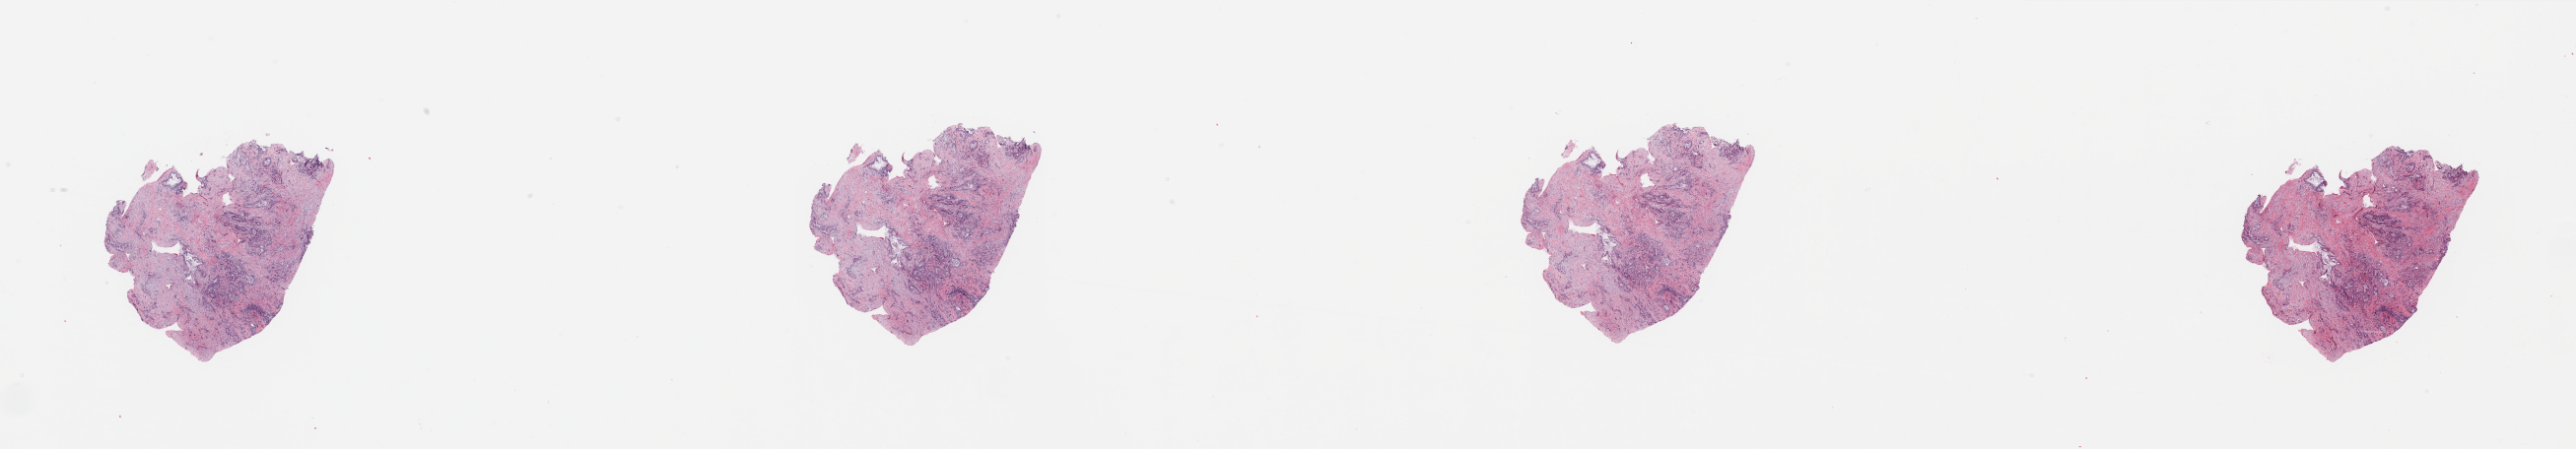
Digitized Hematoxylin and eosin (H&E) stained tissue section (whole slide), shown as a low-resolution overview of the whole scanned area (about 41.3 x 7.2 mm, from a 20x scan), tumour tissue sample, sampled site: pancreas. Patient: female, age 67 years. Histologic grade: G2 (moderately differentiated). Slide review estimates, as recorded: tumour nuclei 60%, necrosis 0%.
Histologic diagnosis: Infiltrating duct carcinoma, NOS. AJCC pathologic stage: IB. Primary tumour site (as recorded): head.